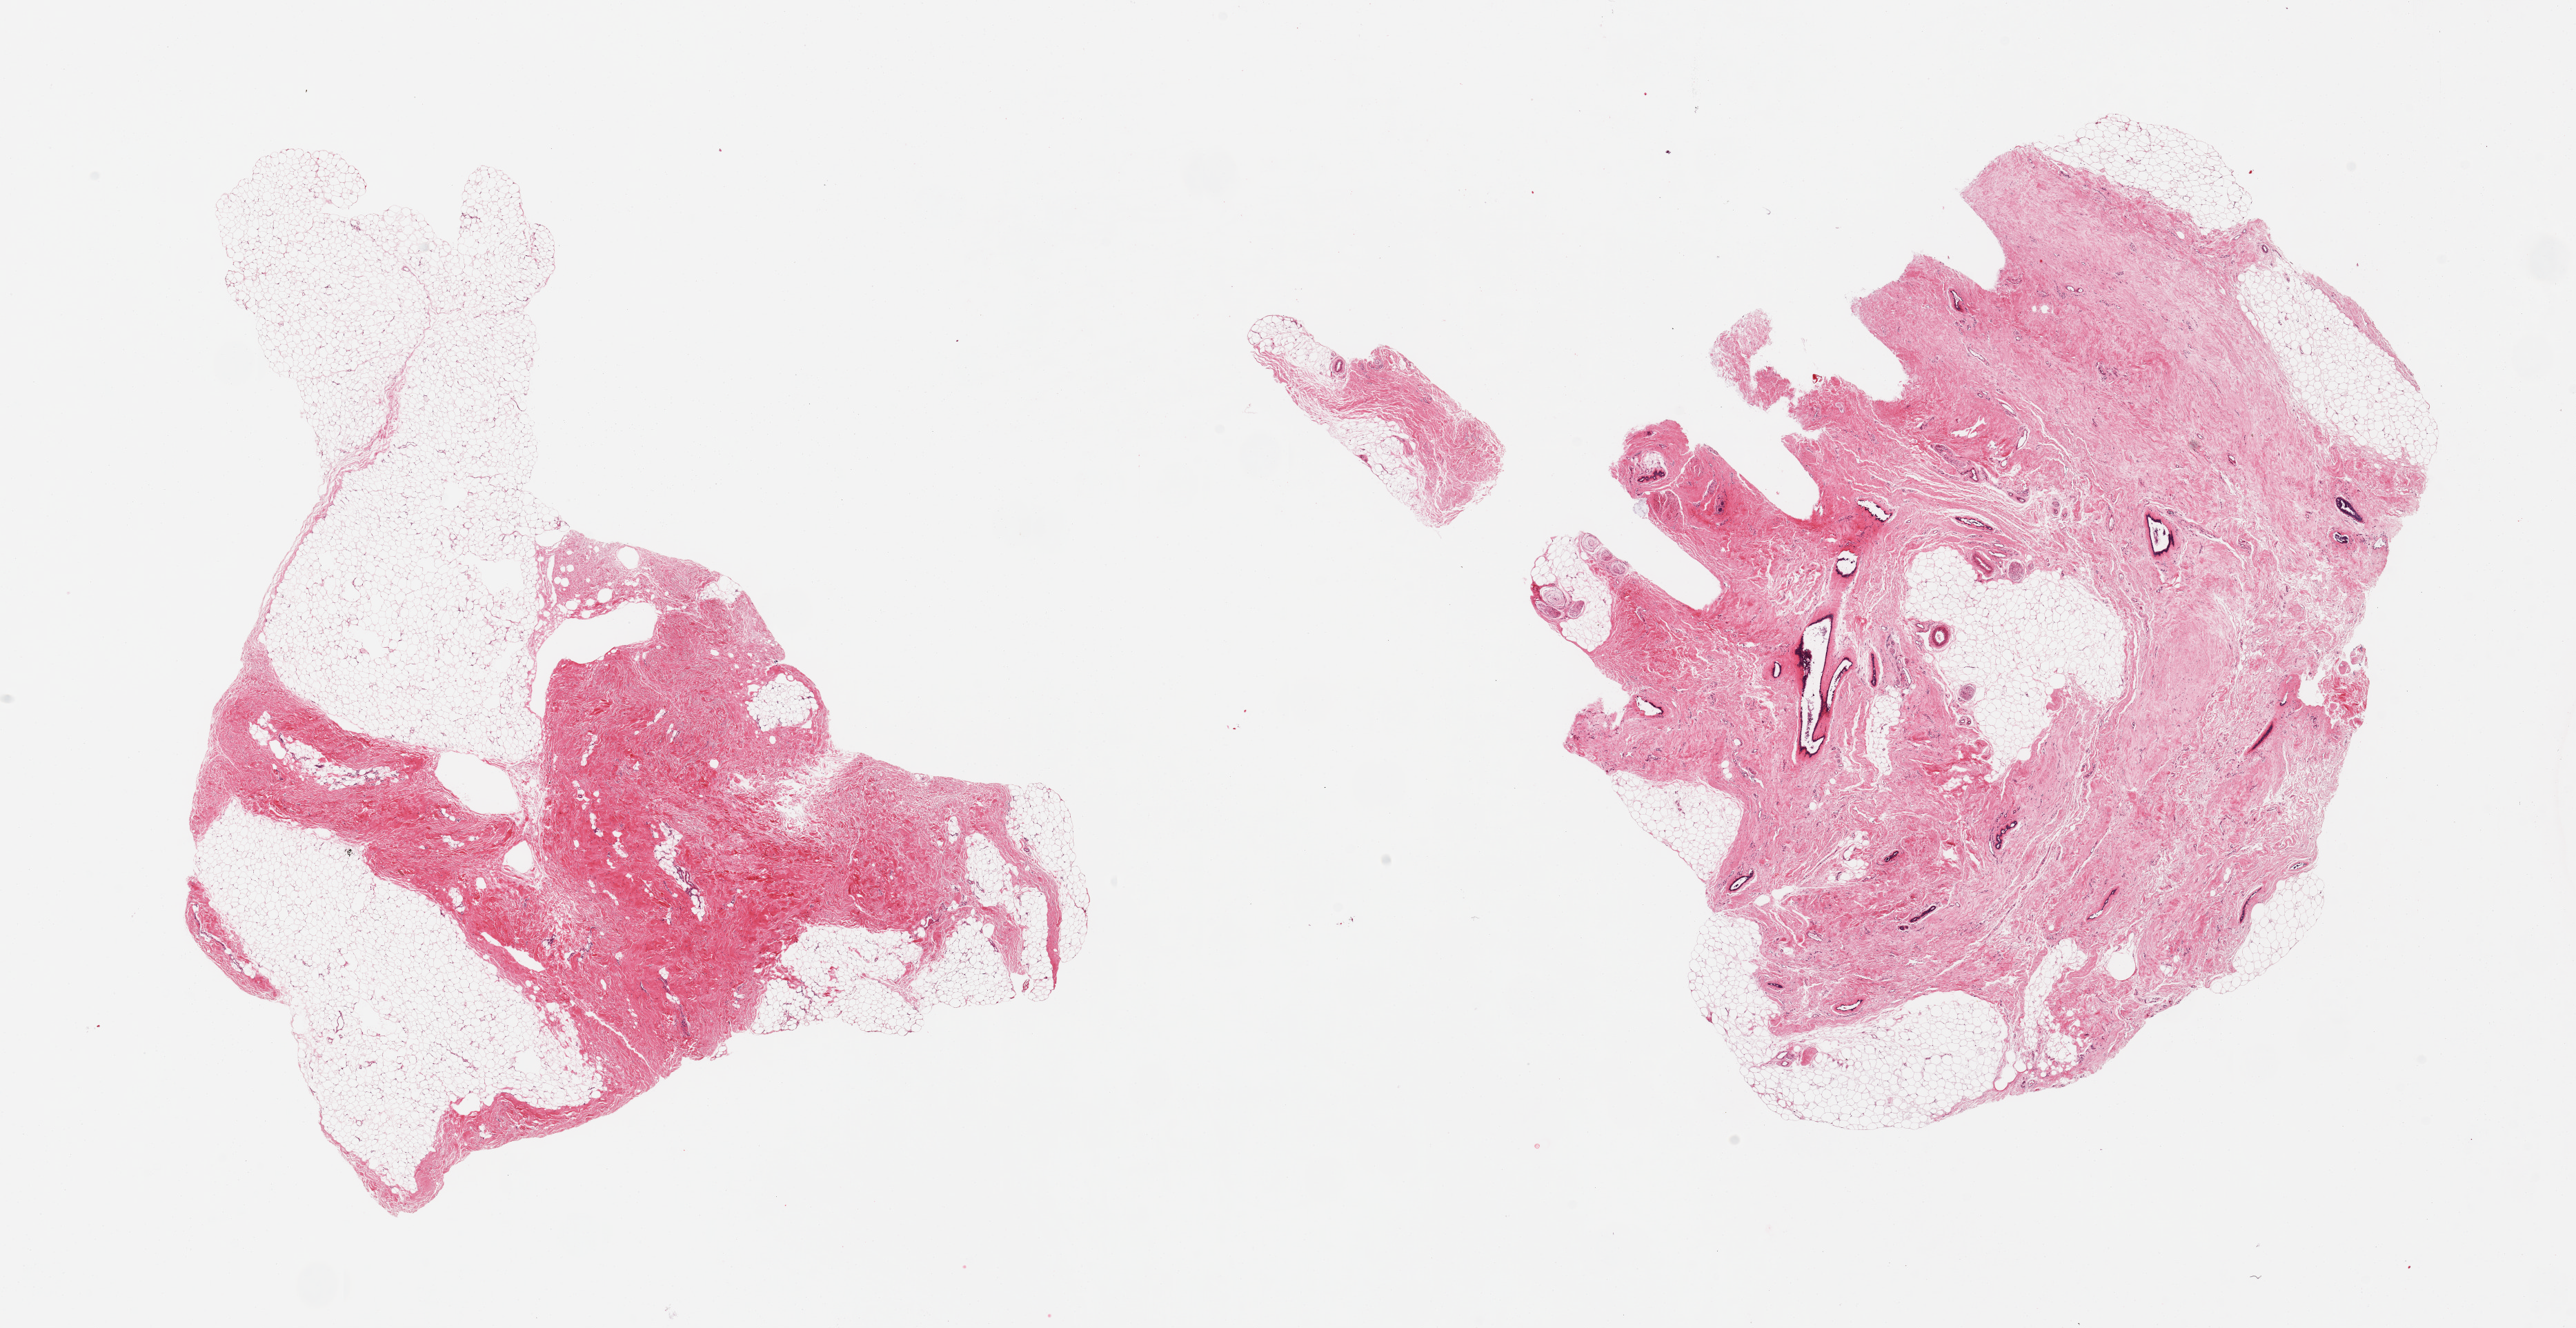
Digitized hematoxylin and eosin (H&E)-stained section, shown as a low-resolution overview of the whole scanned area (about 29.5 x 15.2 mm); PAXgene-fixed paraffin-embedded (PFPE) section; target tissue: breast; donor tissue sample. Donor: male.
Reviewer comment on this tissue sample: 2 pieces; fibrofatty tissue, 1 with several ducts; neural elements.